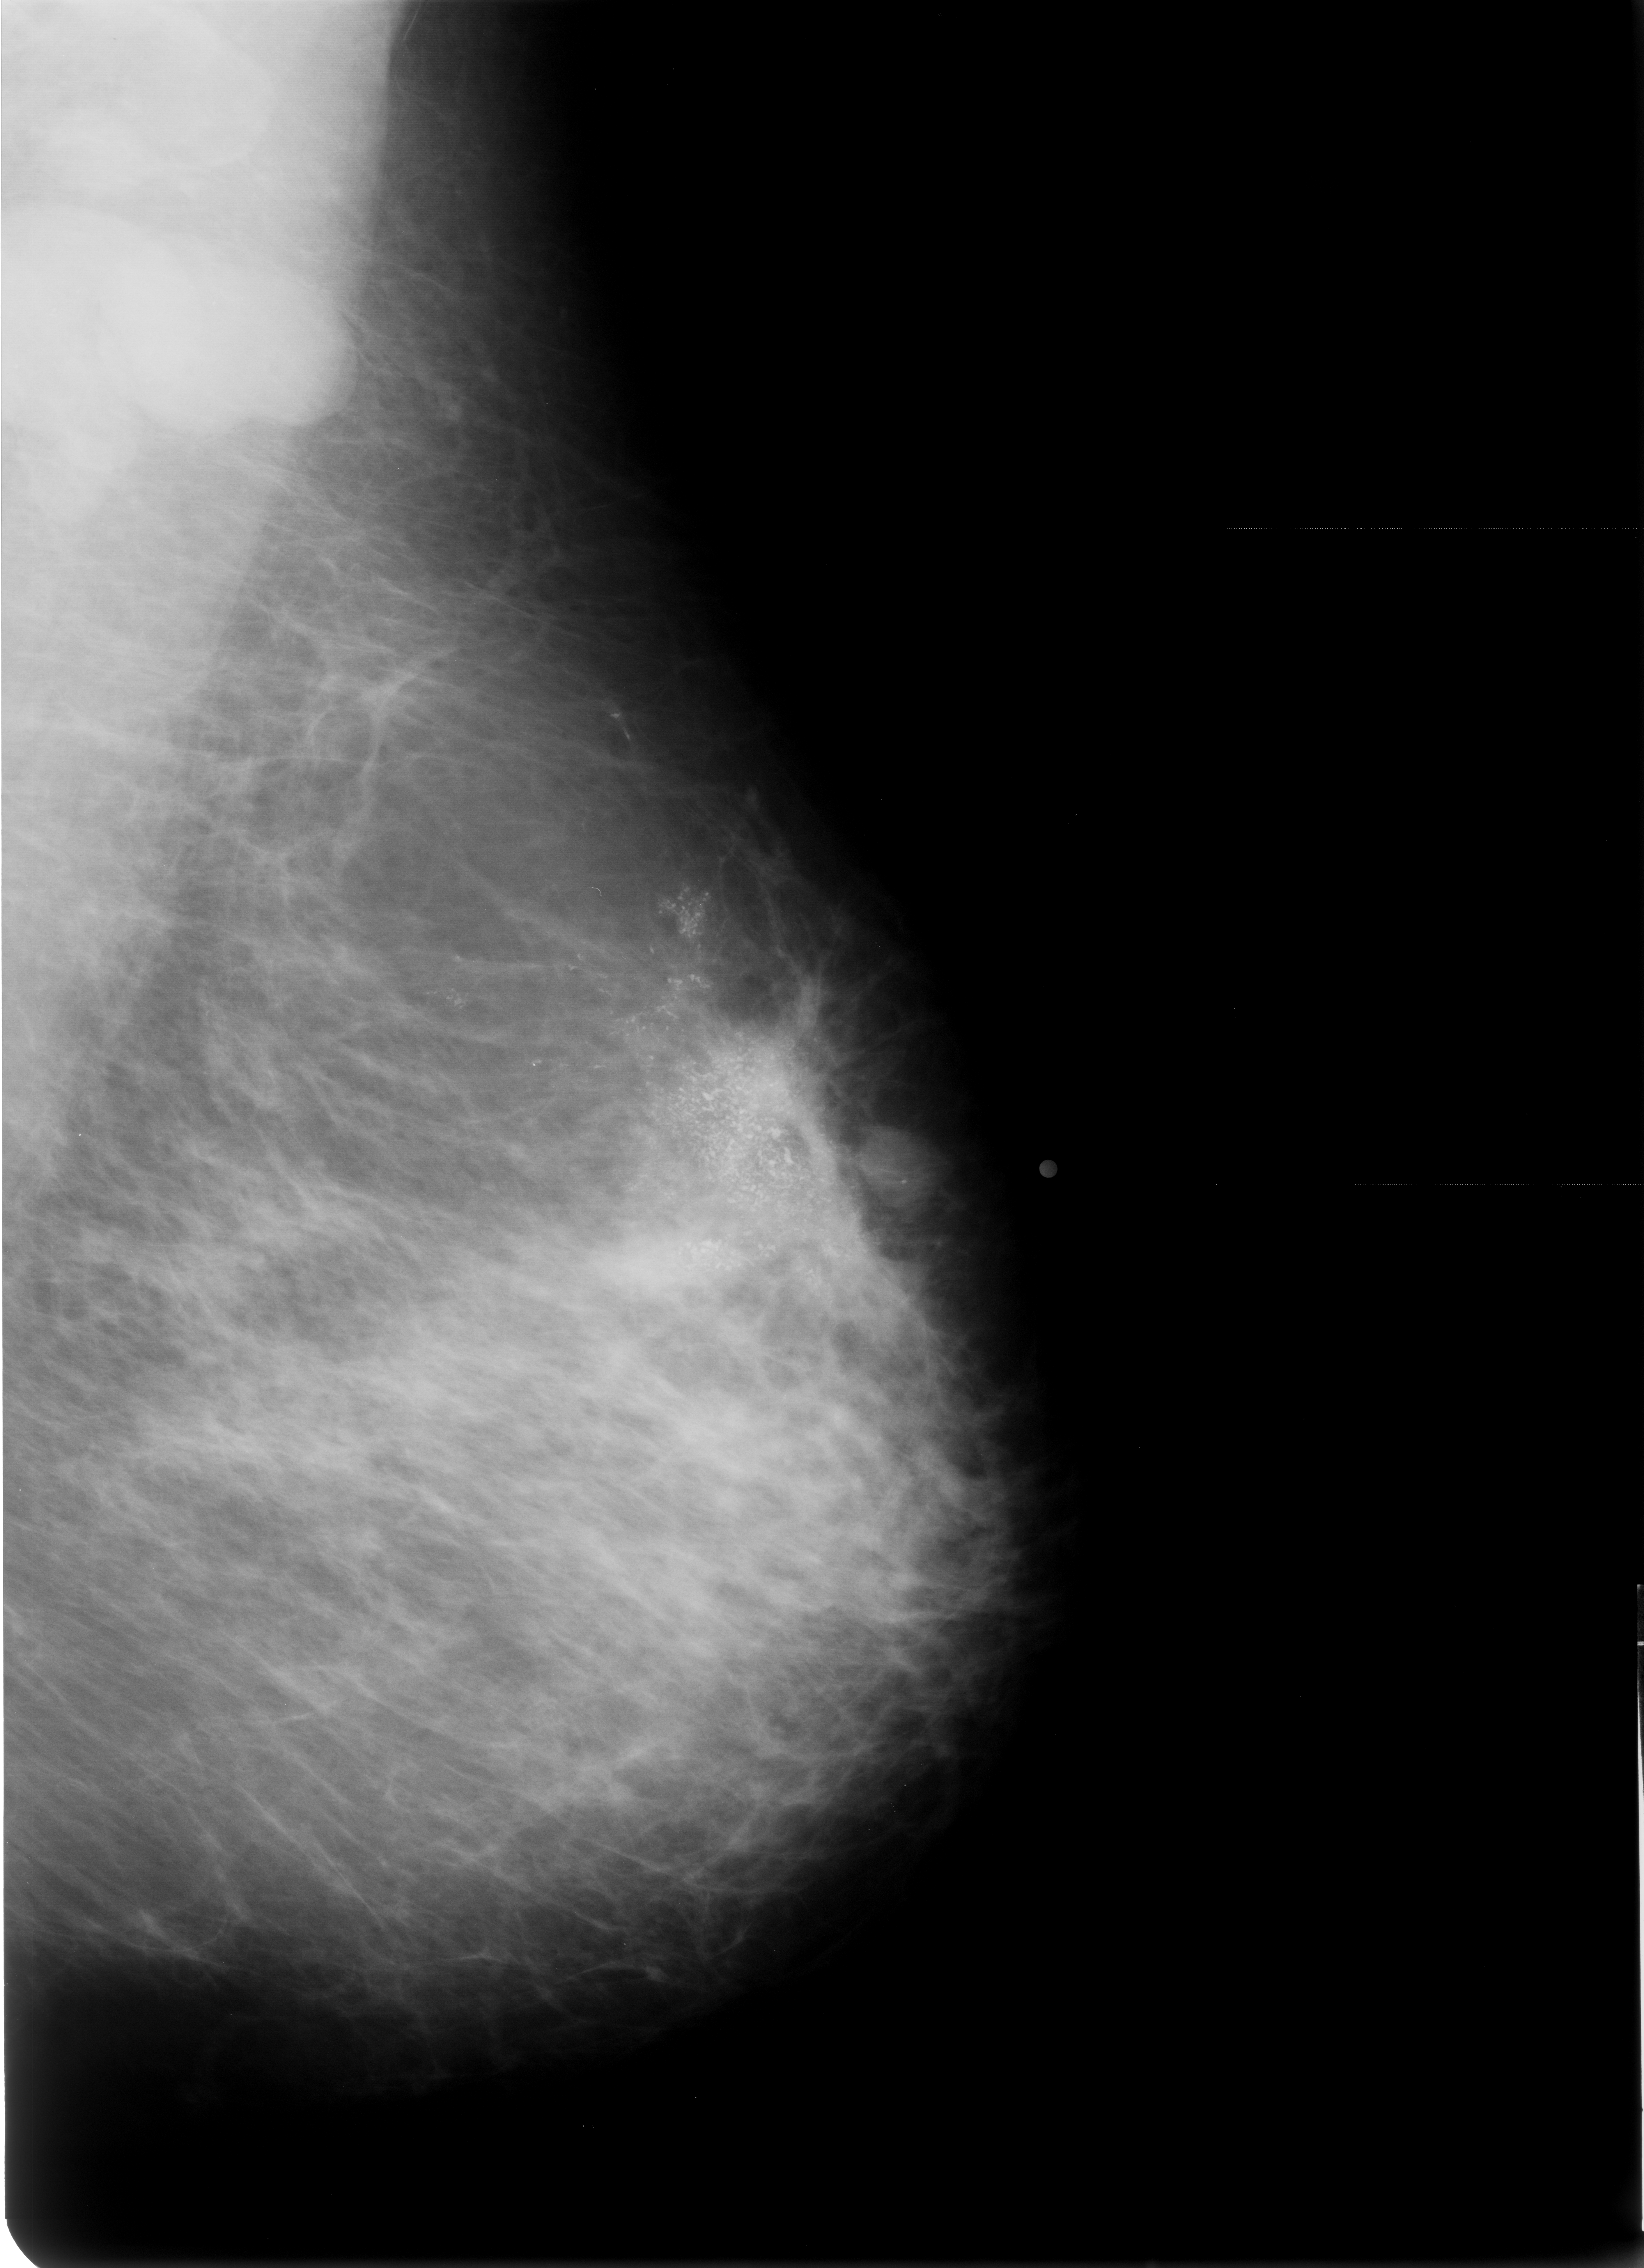
Scanned film-screen mammogram, left breast, mediolateral oblique (MLO) view, BI-RADS breast density category 2 (scale 1–4).
Marked findings (only marked abnormalities are described; nothing is implied about the rest of the image): calcifications, morphology pleomorphic, distribution segmental; BI-RADS assessment category 5; pathology (as recorded): malignant.